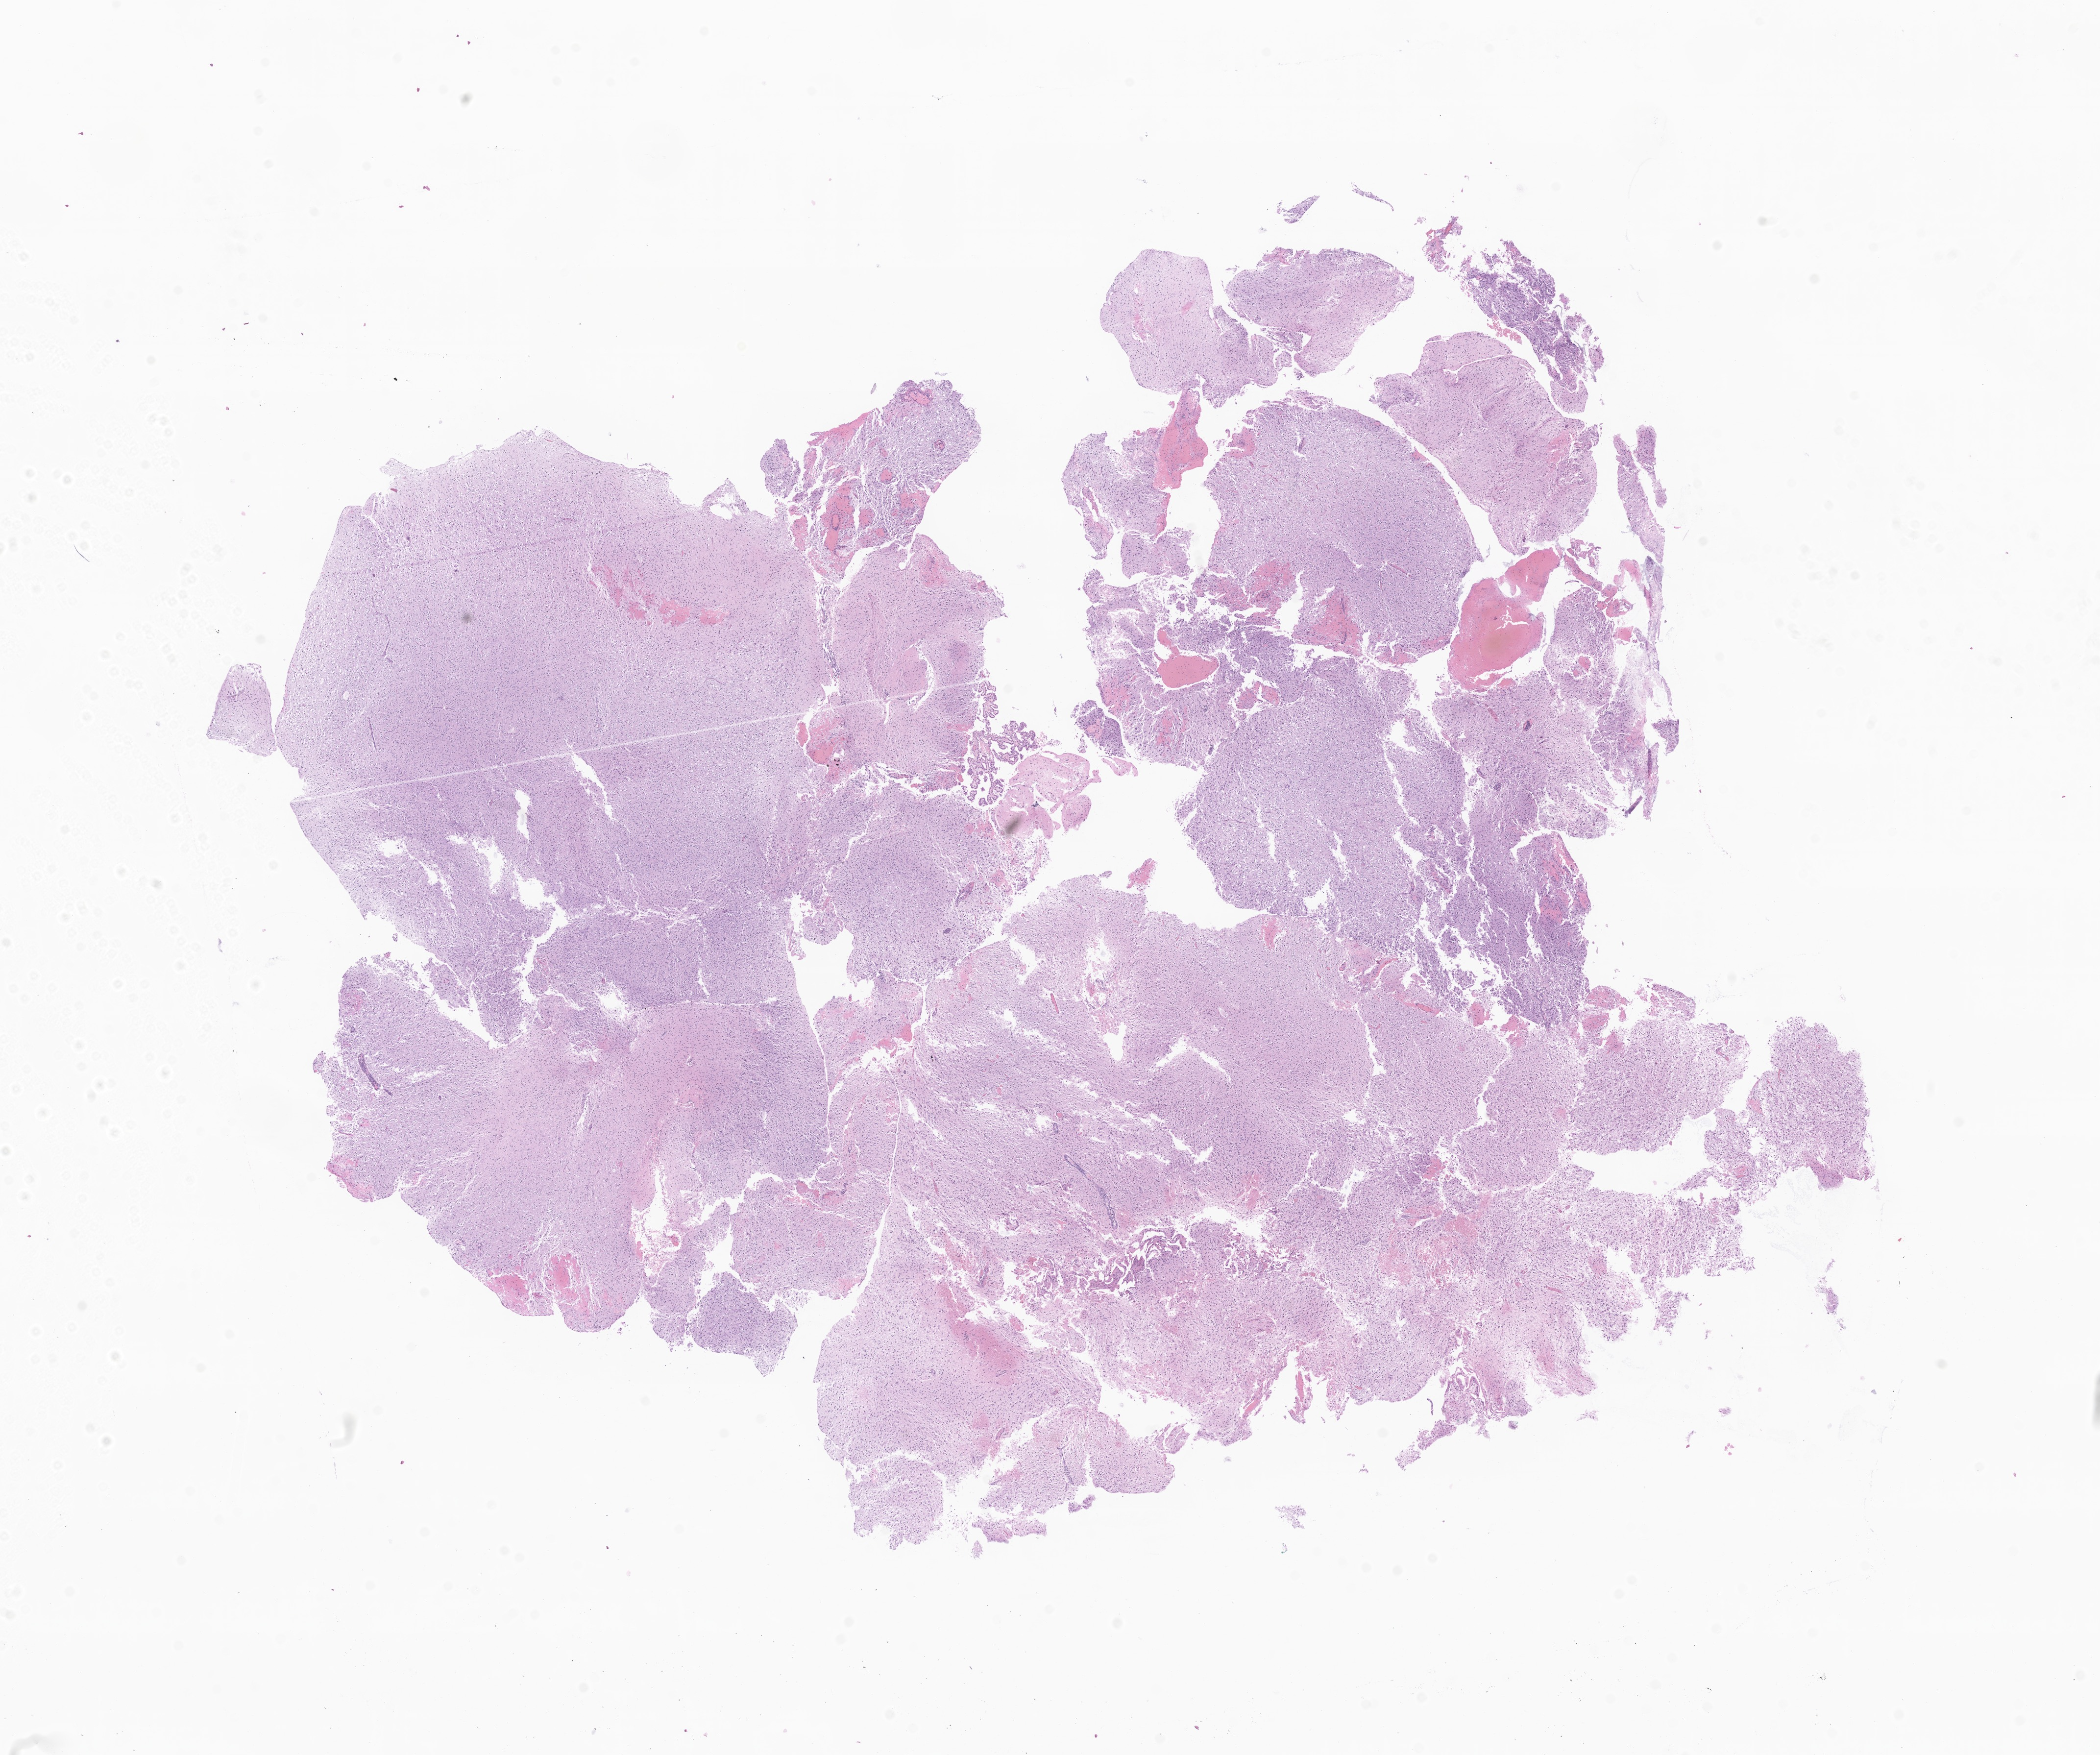
Digitized haematoxylin and eosin-stained section of tumor tissue from the brain, a low-resolution overview of the entire scanned area, about 18.1 x 15.1 mm, formalin-fixed, paraffin-embedded (FFPE) tissue. Patient: female, age 70 months (5 years 10 months).
• diagnosis (ICD-O-3 morphology term): Glioma, malignant